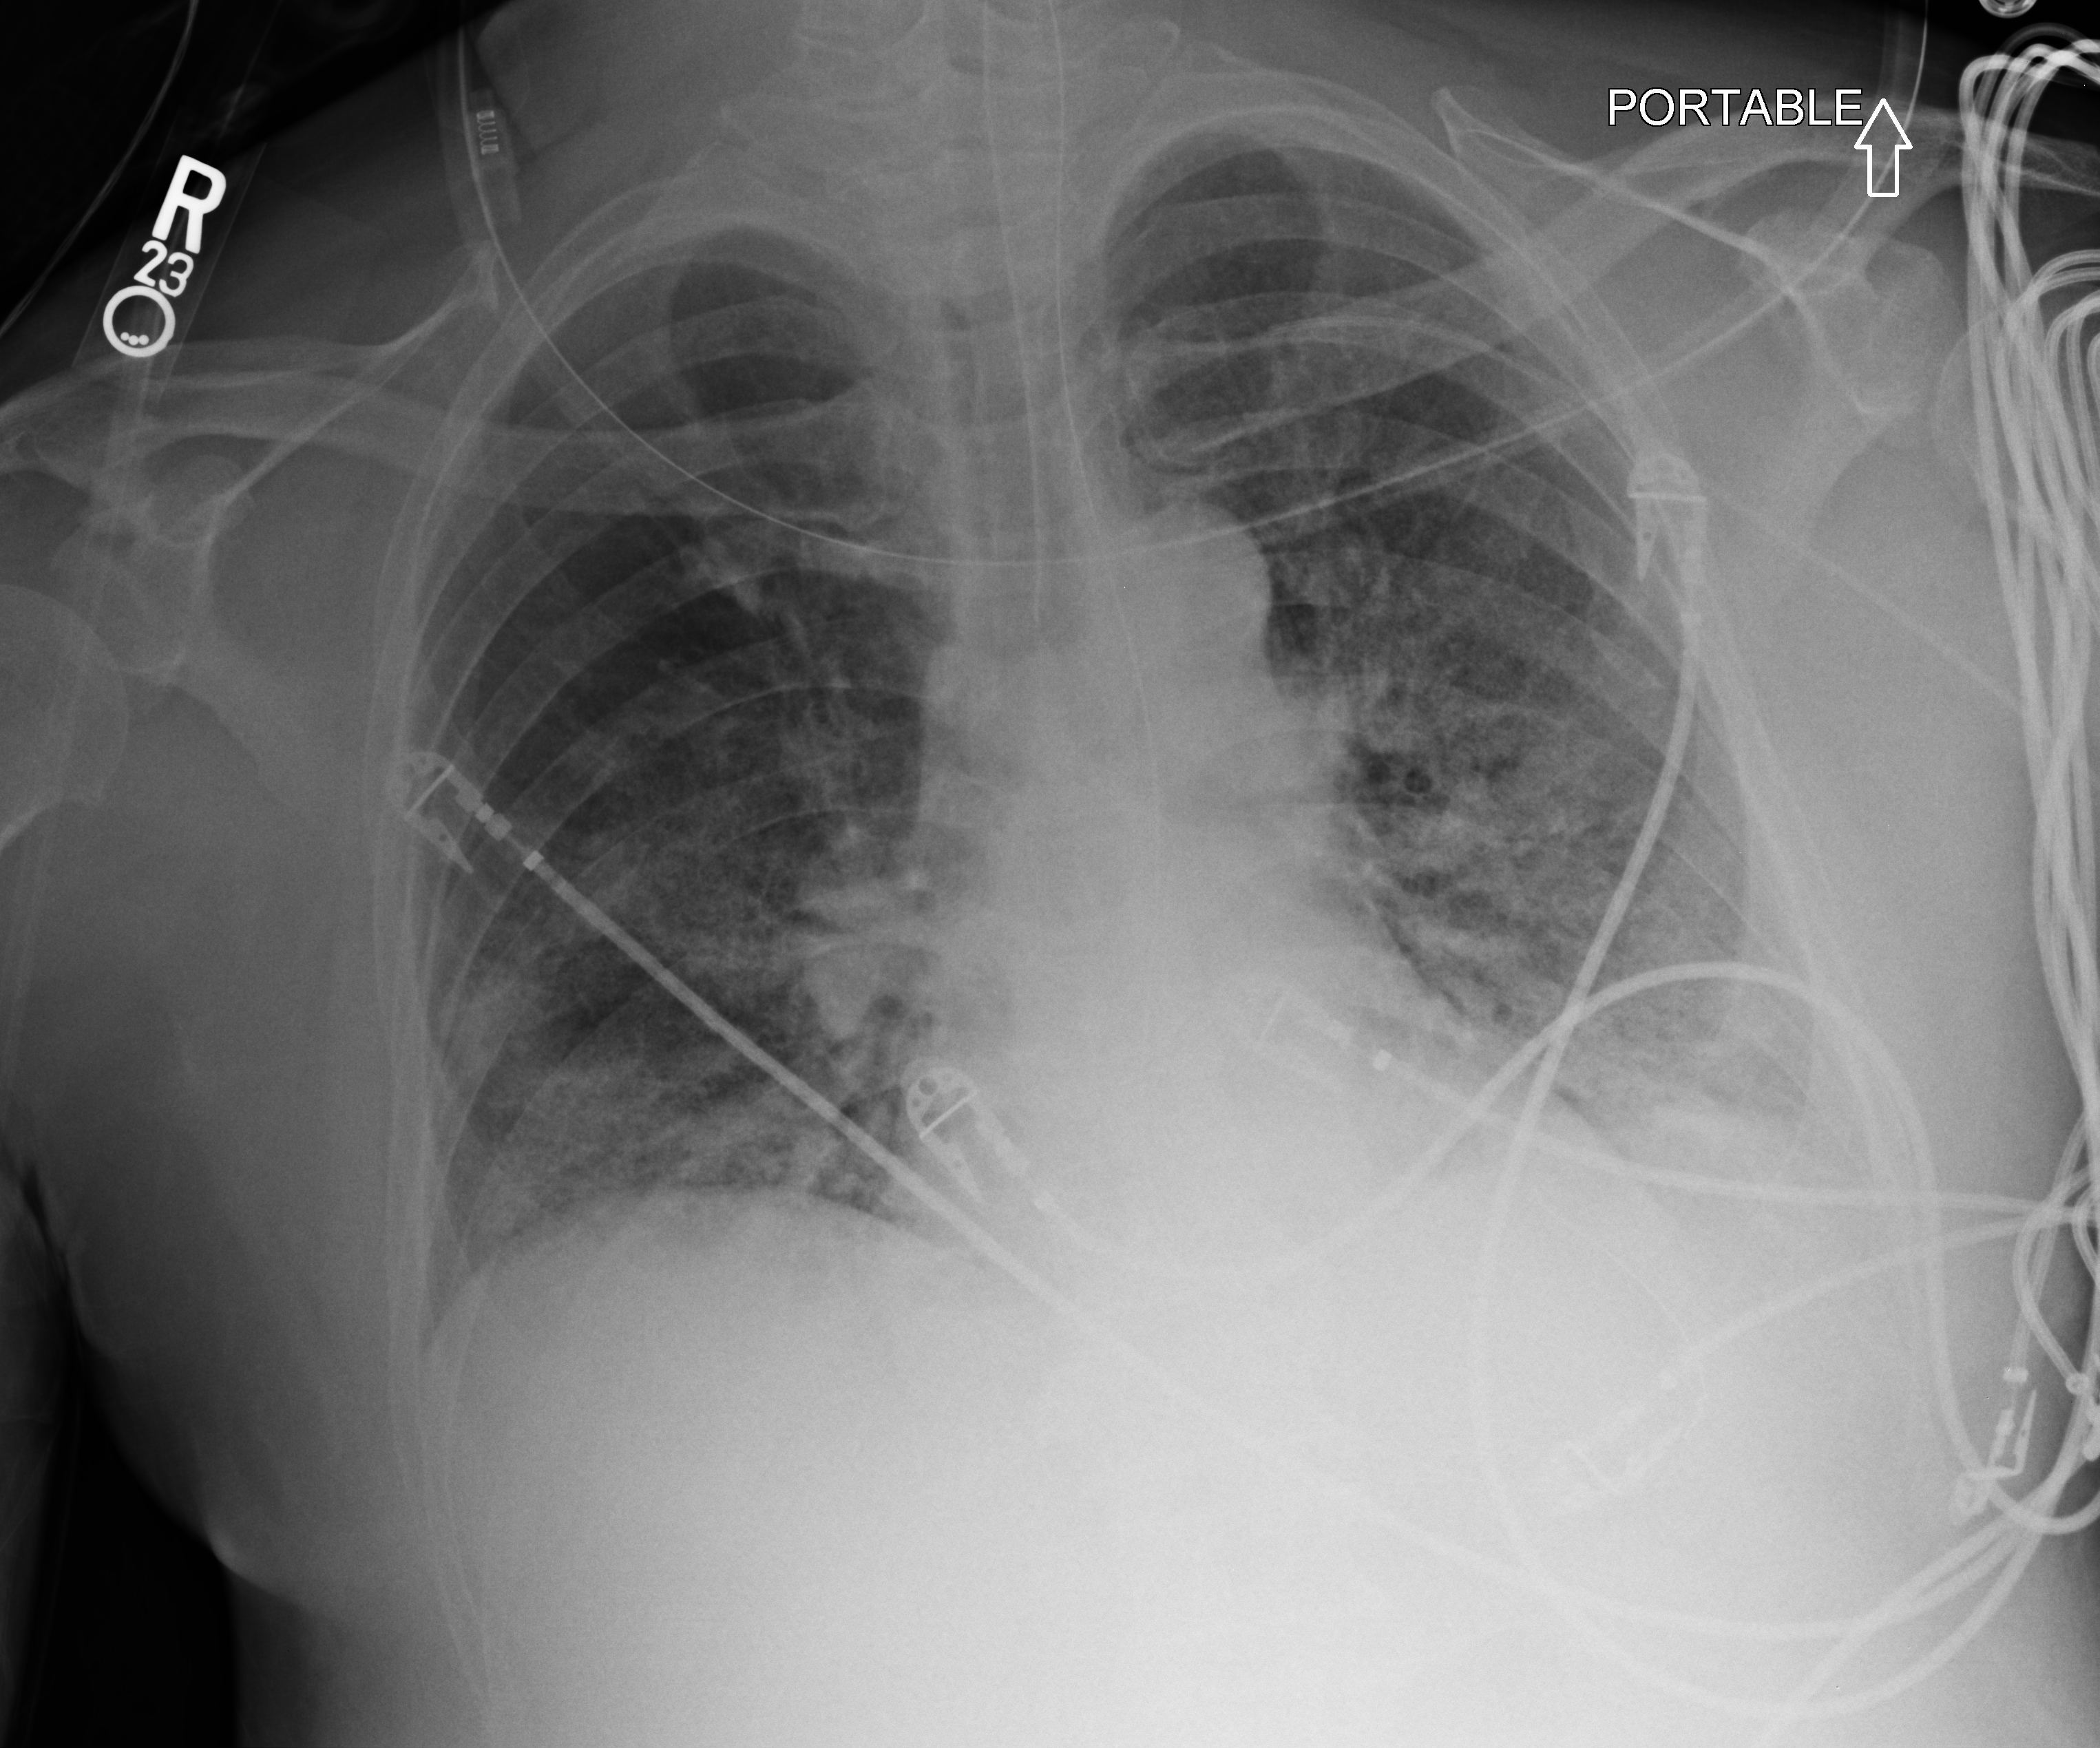
Bedside chest radiograph (computed radiography), anteroposterior (AP) projection. Patient hospitalised with COVID-19; male, aged 60–74 years.
From the hospital-stay record, not from the radiograph (when in the stay this image was taken is not recorded): hypertension (admission record): yes; COPD (admission record): no; mechanically ventilated during this hospital stay: yes.